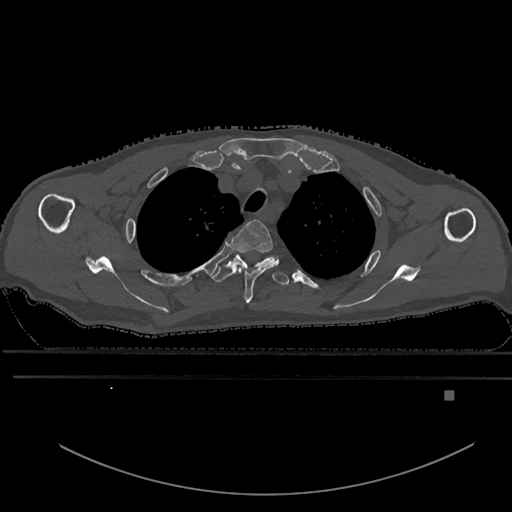
CT including the spine, one axial slice; slice 476 of 969 in the series (ordered by position); bone window (W 1800 / L 400 HU); 0.5 mm slice thickness; 512 × 512 image matrix, field of view 456 × 456 mm. Patient: male, 82 years. Case-level facts recorded for this patient, not image findings: primary cancer: prostate; vertebrae with lytic lesions (as recorded): T11, T9, T8, T2.
Annotated regions visible in this slice (semi-automatic segmentation, software-assisted and operator-edited):
- T2 vertebra: bounding box [x1, y1, x2, y2] px = [231, 219, 279, 304]
- T3 vertebra: [211, 252, 289, 286]